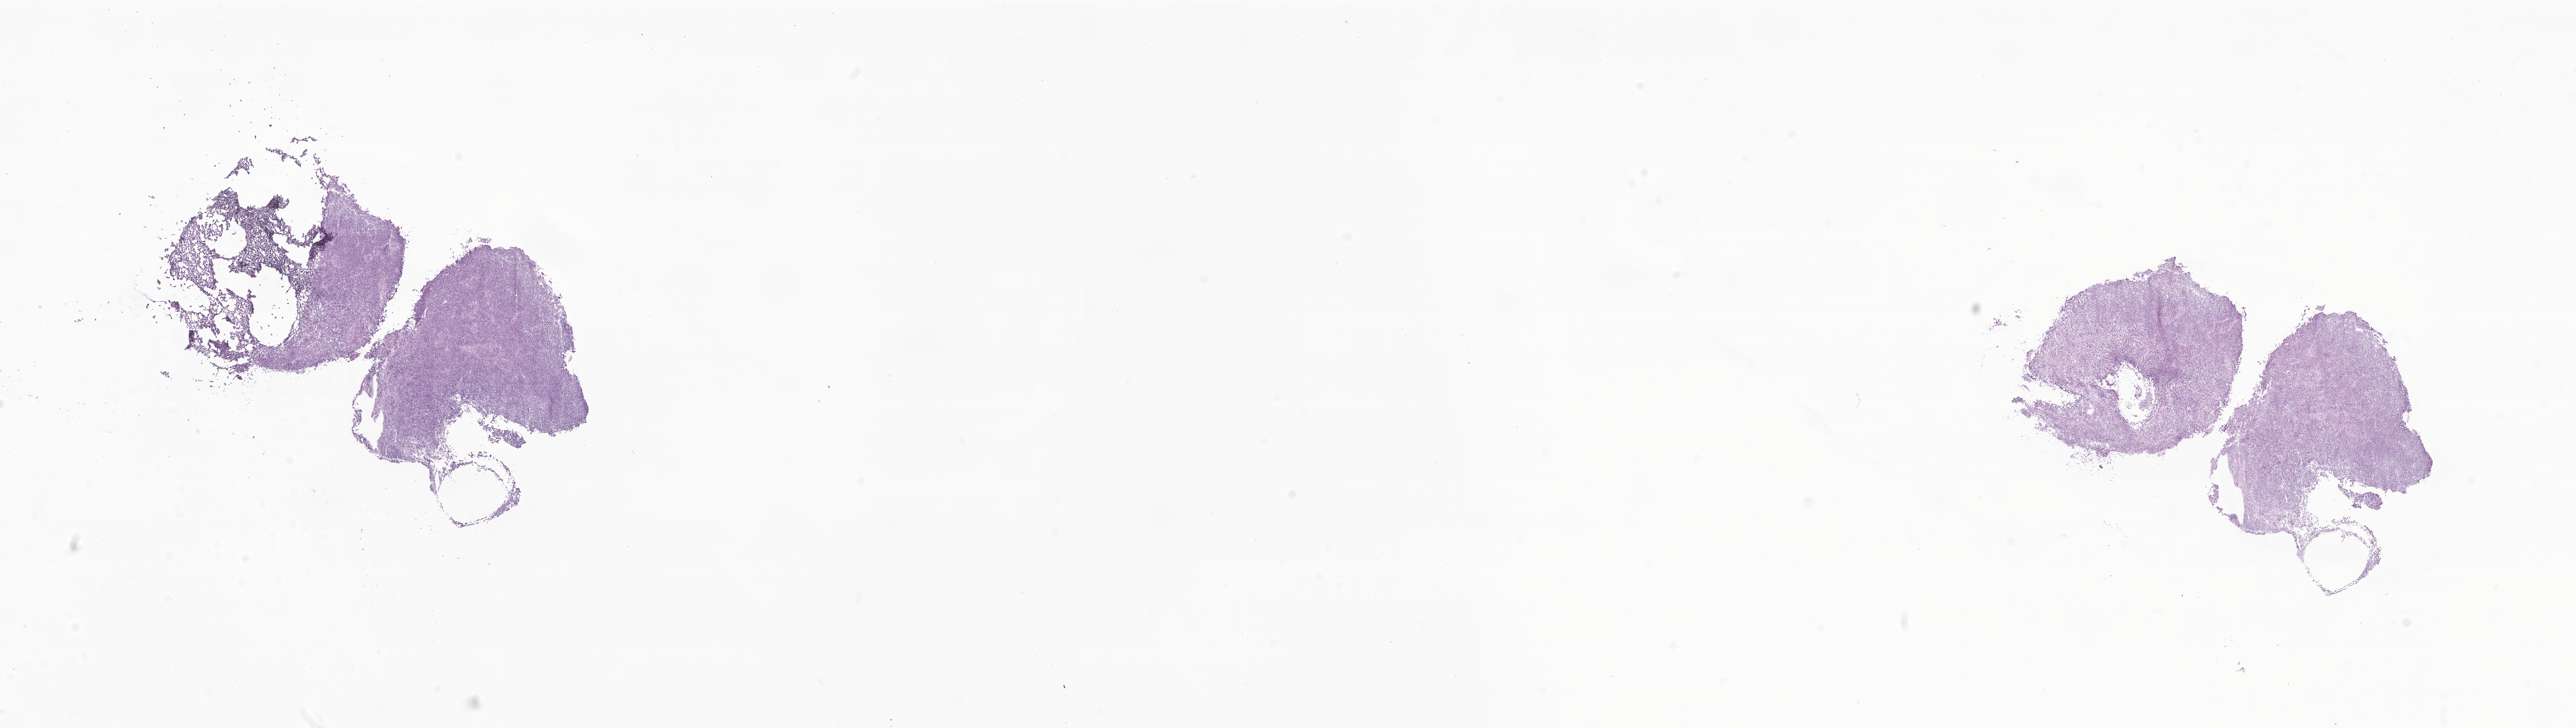
Digitized hematoxylin and eosin (H&E)-stained section of tumor tissue from the brain, whole scanned area (about 32.8 x 9.3 mm) shown as a low-resolution overview. Cryosection (OCT / tissue freezing medium). Patient female; age 607 days (about 1.7 years).
Diagnosis (ICD-O-3 morphology term): Neoplasm, malignant.